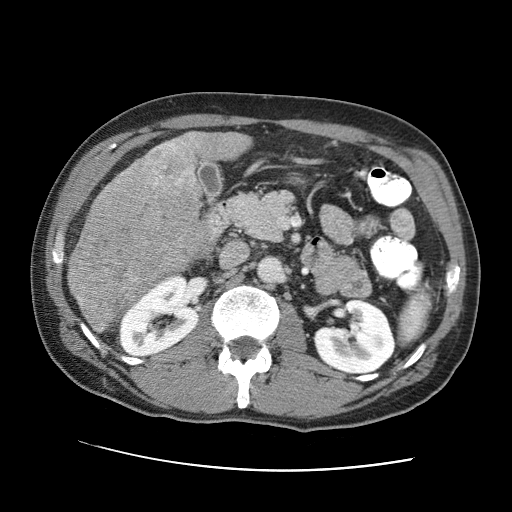
Contrast-enhanced abdominal CT (liver protocol), one axial slice; reconstruction kernel STANDARD; one of 2 acquisitions stored at this slice position; soft-tissue window (W 400 / L 40 HU); 512 × 512 image matrix. From the clinical record (not read from this slice): diagnosis: hepatocellular carcinoma (patient treated with transarterial chemoembolisation; whether this scan precedes or follows treatment is not stated here); TNM stage (as recorded): Stage-IVA.
Structures marked on this image (semi-automatic segmentation, software-assisted and operator-edited):
- liver parenchyma outside the tumour (the mass and vessels are separate outlines, so this box may not span the whole liver): bounding box (x1, y1, x2, y2) in pixels: (68, 132, 248, 305)
- mass: (67, 139, 210, 335)
- liver vessels: (181, 137, 191, 145)